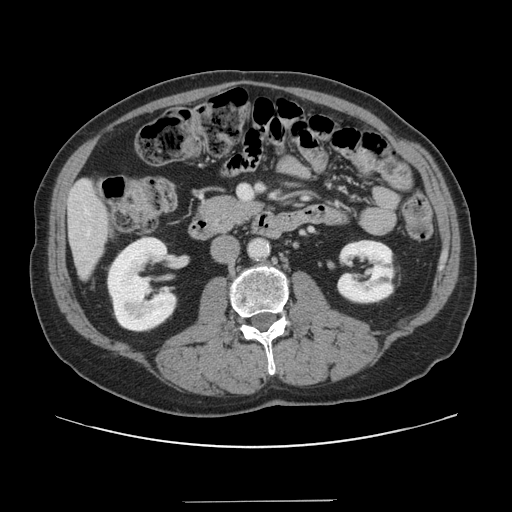
Contrast-enhanced abdominal CT, one axial slice. Slice 46 of 151 in the series (ordered by position). 120 kVp. Soft-tissue window (W 400 / L 40 HU). 512 × 512 image matrix, field of view 399 × 399 mm. Male patient, age 63 years. From the clinical record (not read from this slice): diagnosis: colorectal cancer liver metastases, imaged before liver resection; multiple liver metastases: no; largest metastasis: 2.1 cm; chemotherapy before resection: no.
Structures marked on this image (outlined manually by an expert reader):
- liver: box from (x=69, y=182) to (x=110, y=276) px
- planned liver remnant (the part of the liver to remain after resection): (x=69, y=182)–(x=111, y=276)
- portal vein (with intrahepatic branches): (x=239, y=185)–(x=251, y=199)